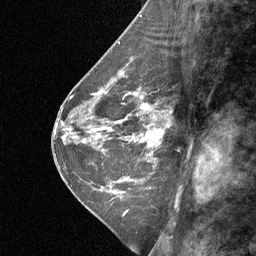
Breast MRI (dynamic contrast-enhanced), one sagittal slice. Slice 26 of 64 in the series (ordered by position). Dynamic contrast-enhanced study with each time point stored as its own series, time point 2 of 3 at this slice position (early post-contrast, ordered by acquisition time). 1.5 T. TE 4.8 ms, TR 27 ms. 2 mm slice thickness. 256 × 256 image matrix. Patient: female, 42 years. From the clinical record (not read from this slice): setting: breast cancer imaged before/during neoadjuvant chemotherapy; receptor status: triple-negative.
Outlined on this slice (semi-automatically segmented with operator editing):
- analysis volume of interest (the breast-tissue region the enhancement analysis was run in; not a lesion): bounding box <124,94,169,161> (left, top, right, bottom; pixels)
- tumour enhancement mask (voxels above the 90 % enhancement threshold inside the analysis volume of interest): <145,105,164,147>